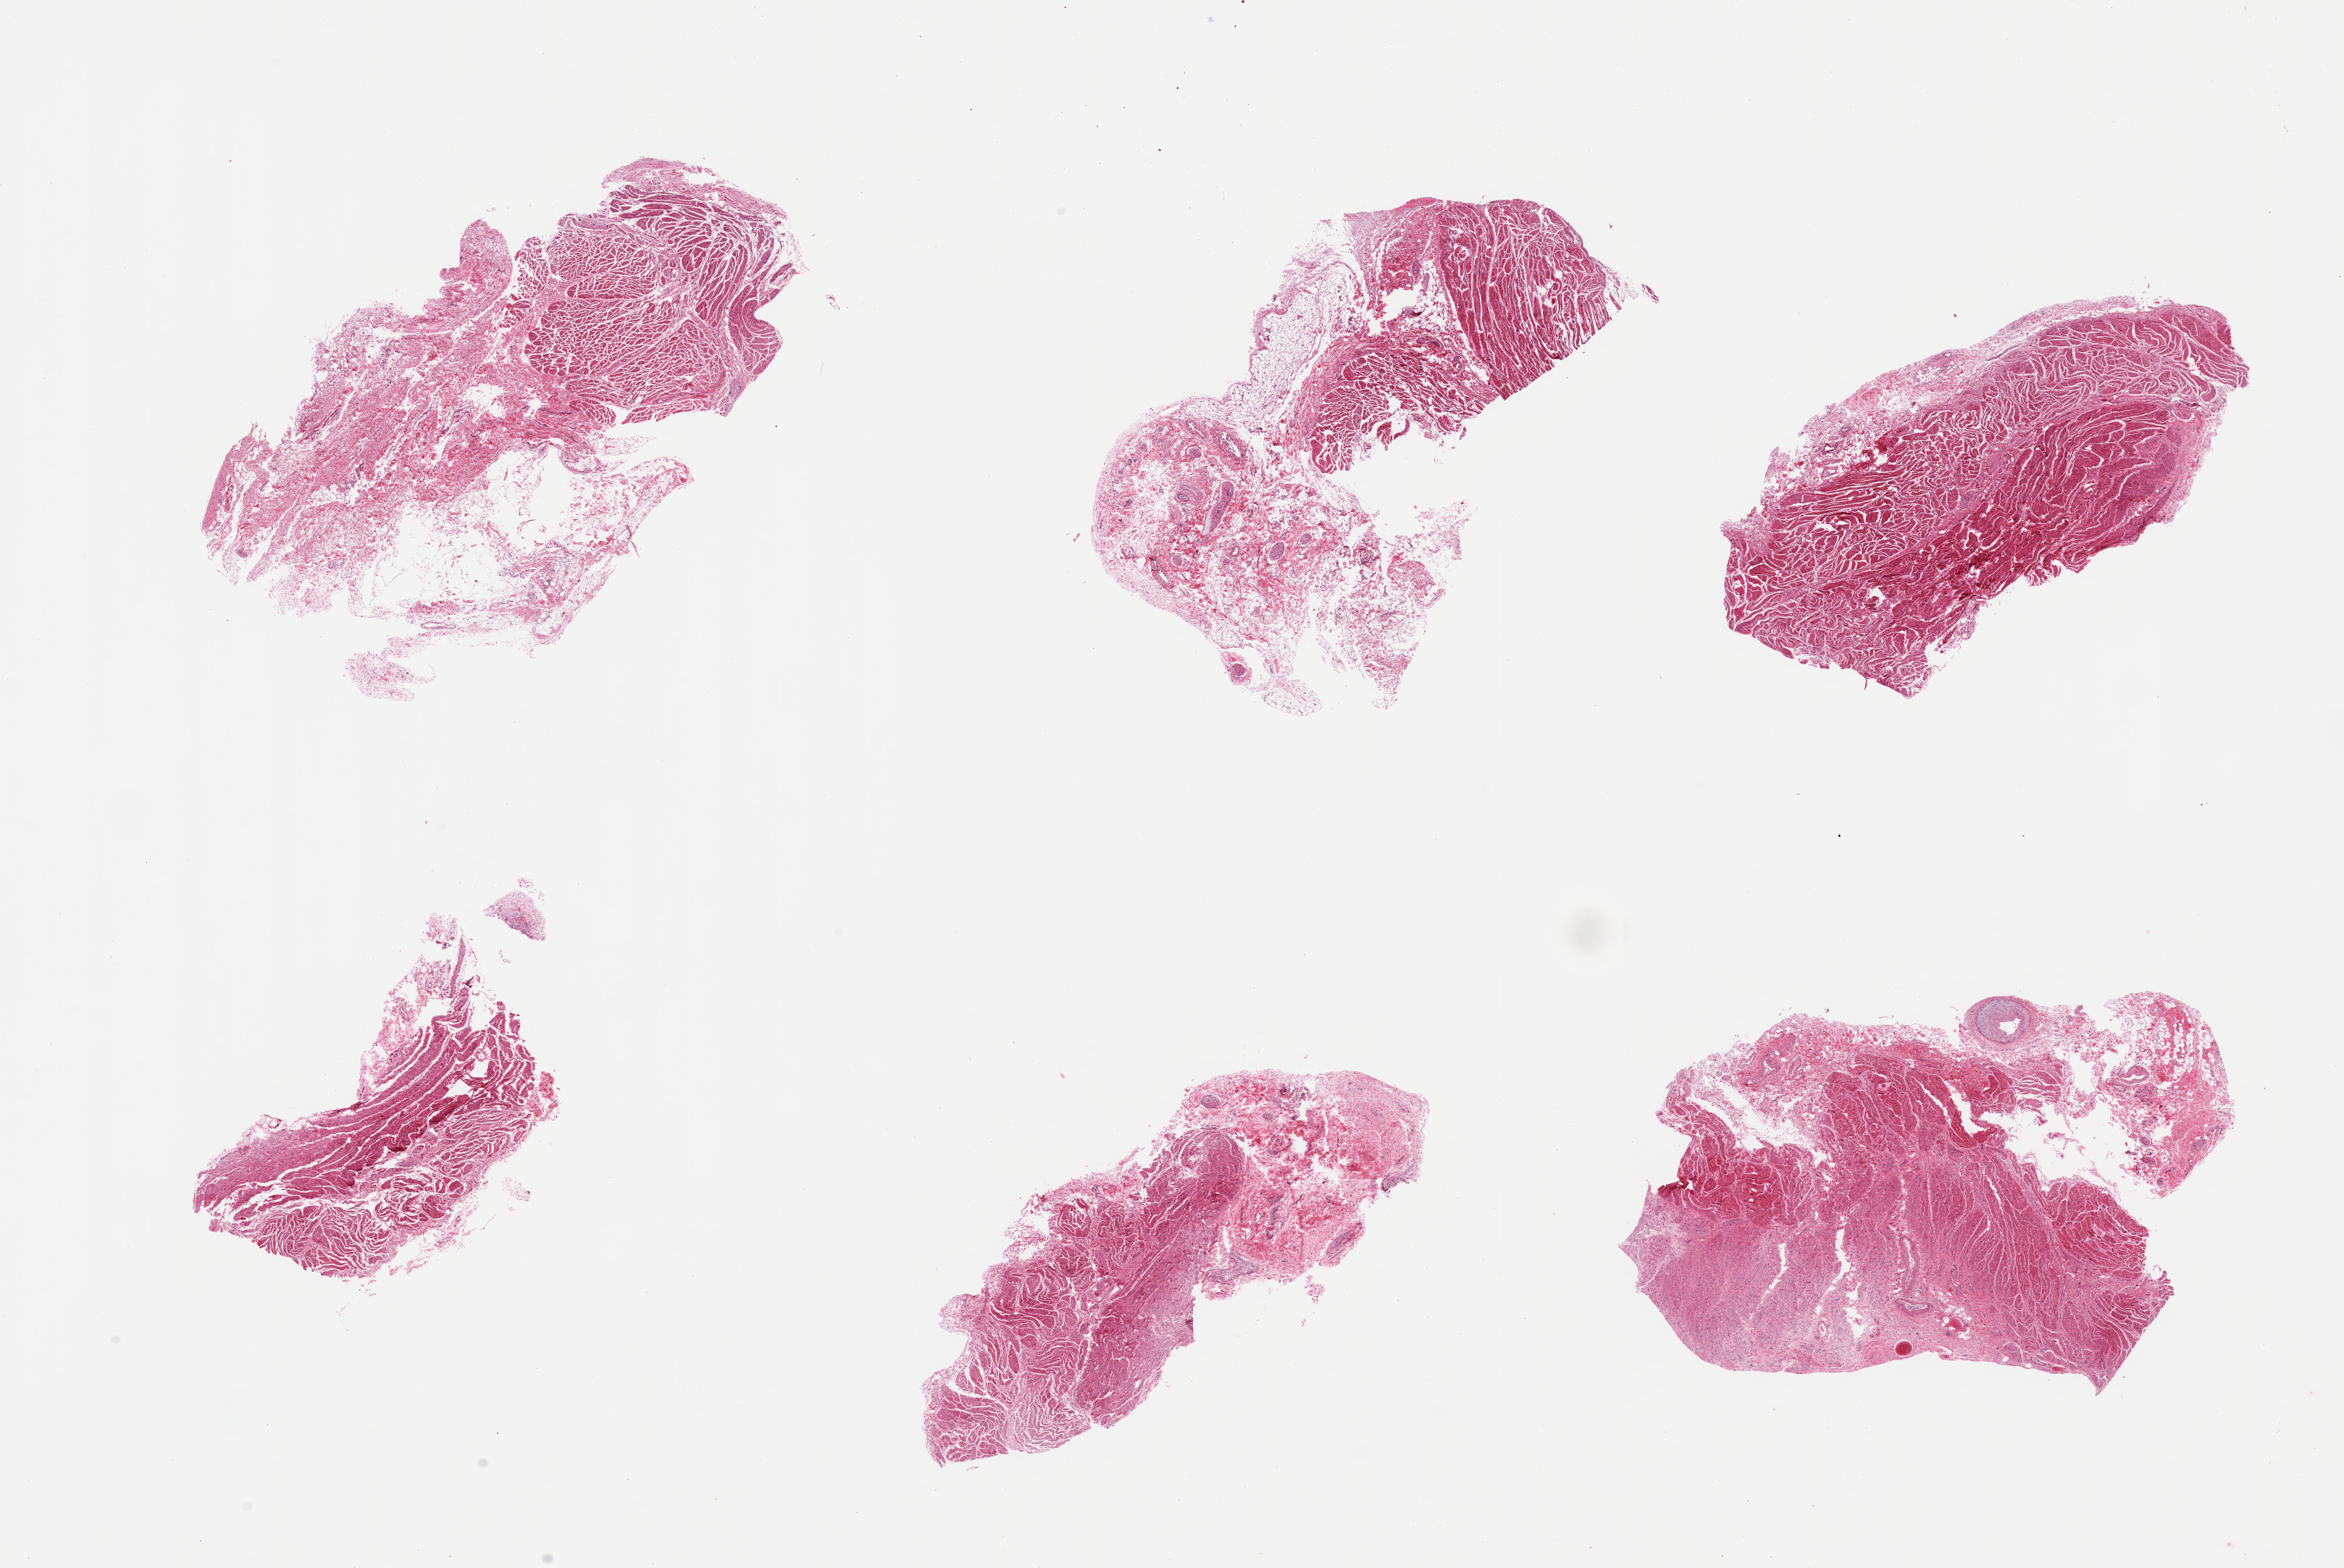
Hematoxylin and eosin (H&E) whole-slide image, shown as a low-resolution overview of the whole scanned area (about 25.6 x 17.1 mm, slide scanned at 20x); PAXgene-fixed, paraffin-embedded tissue; section of esophageal muscle (target tissue); tissue donor sample. Donor: female.
Review note (as recorded): 6 pieces.